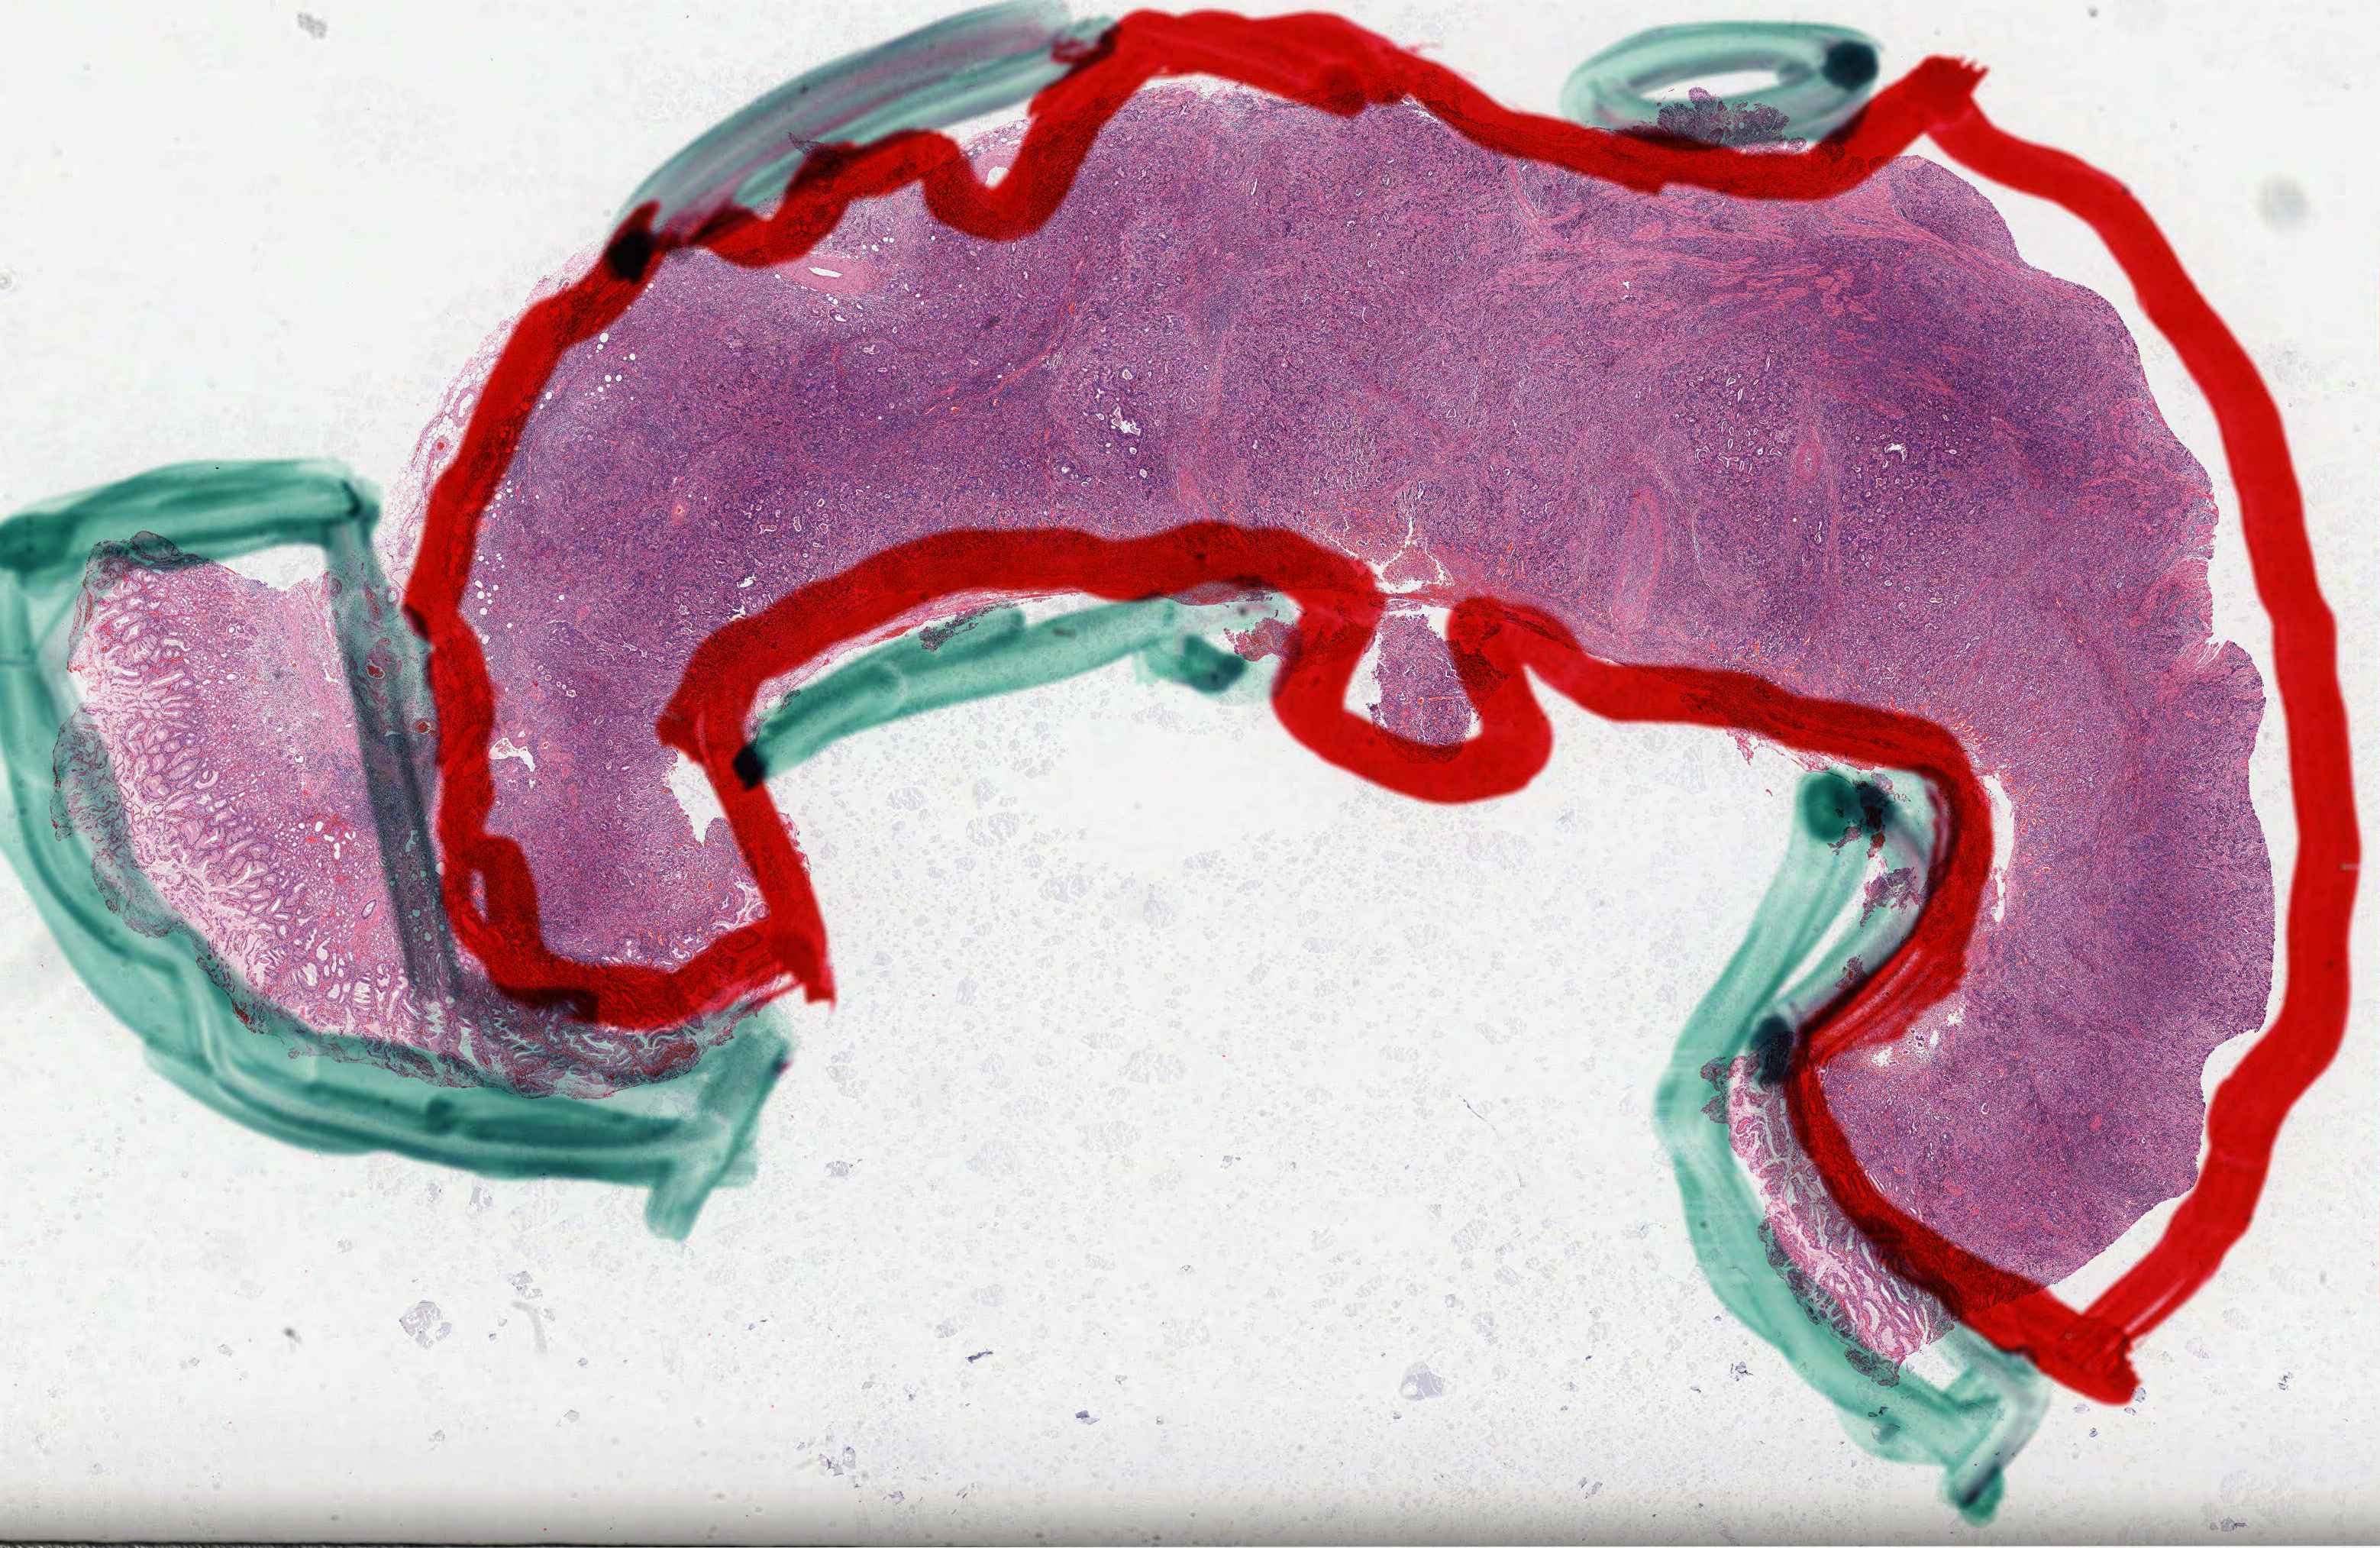
Digitized Hematoxylin and eosin (H&E) stained tissue section (whole slide), low-resolution overview of the scanned area, about 25.1 x 16.3 mm; formalin-fixed paraffin-embedded (FFPE) diagnostic section; stomach, primary tumour sample. Male patient; age at initial diagnosis 60 years. Histologic grade: G3 (poorly differentiated).
Histologic diagnosis: Adenocarcinoma, NOS (body of stomach). AJCC pathologic stage: IIIB (7th edition). Lymph nodes positive (case pathology): 0 of 4 examined.